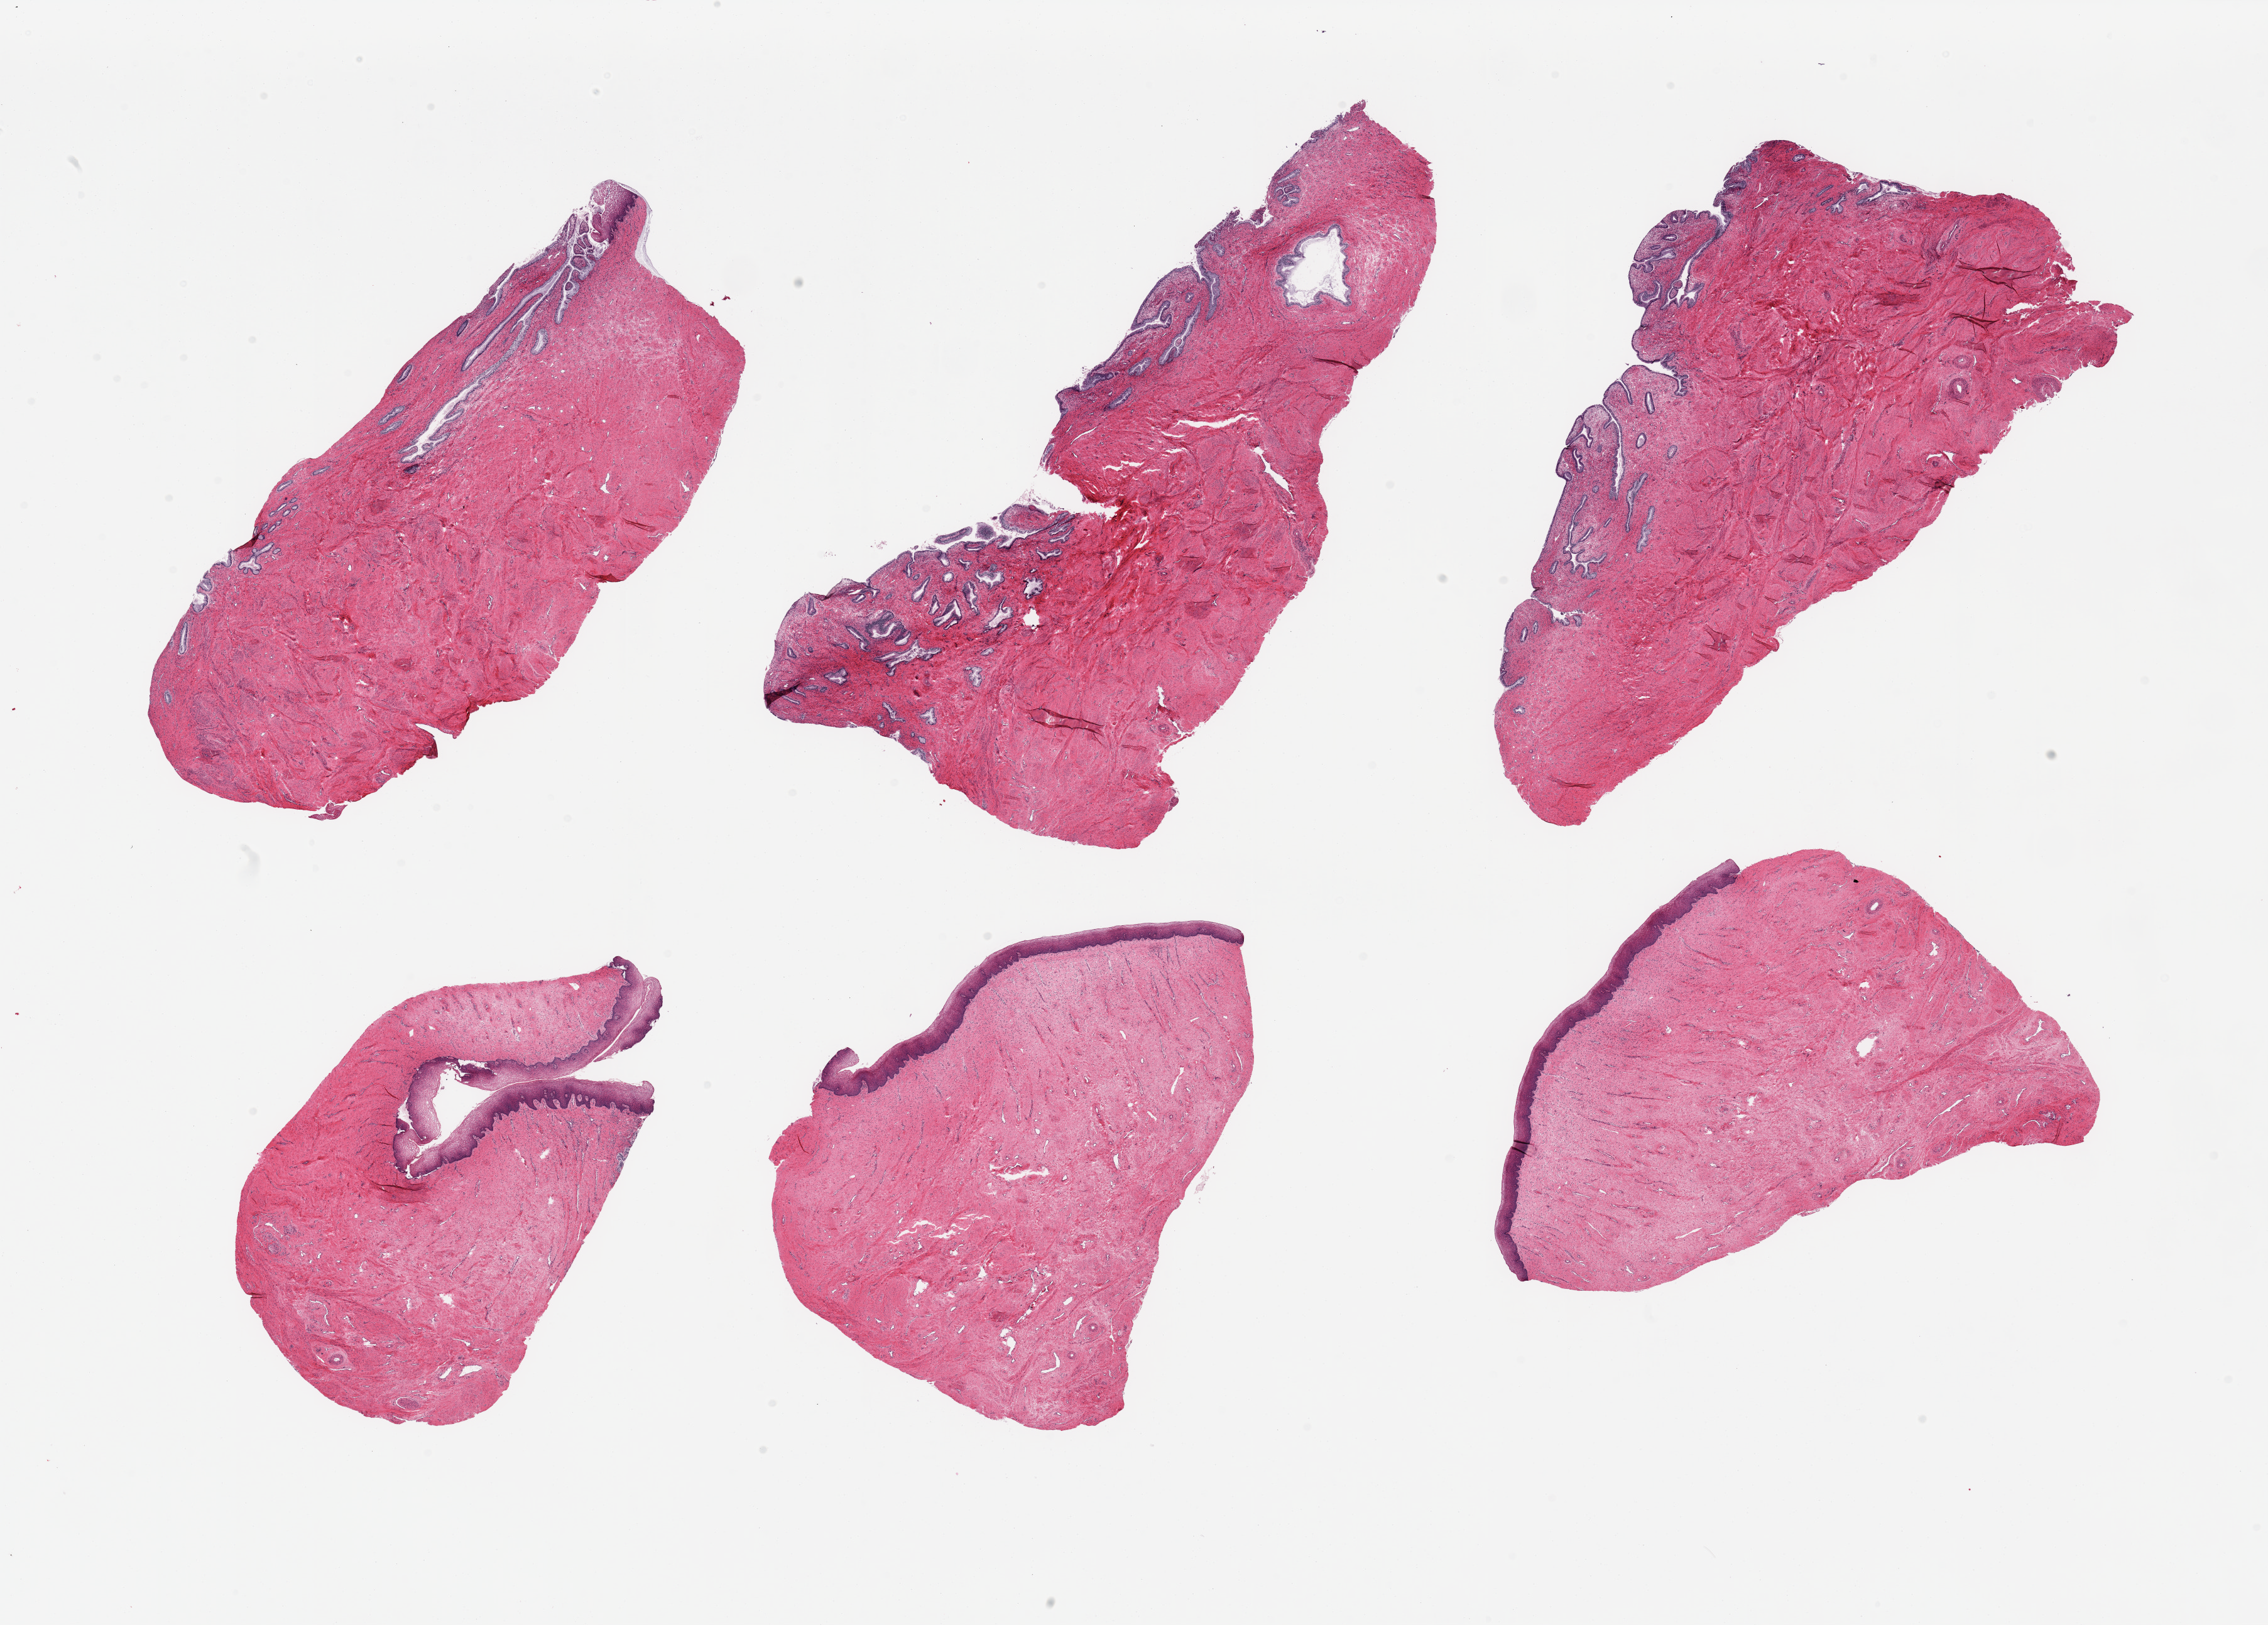
Whole-slide image, H&E stain, brightfield, shown as a low-resolution overview of the whole scanned area (about 28.5 x 20.5 mm, acquisition: 20x scan). Female donor.
Specimen: PAXgene-fixed paraffin-embedded (PFPE) section; section of vagina (target tissue); tissue donor sample.